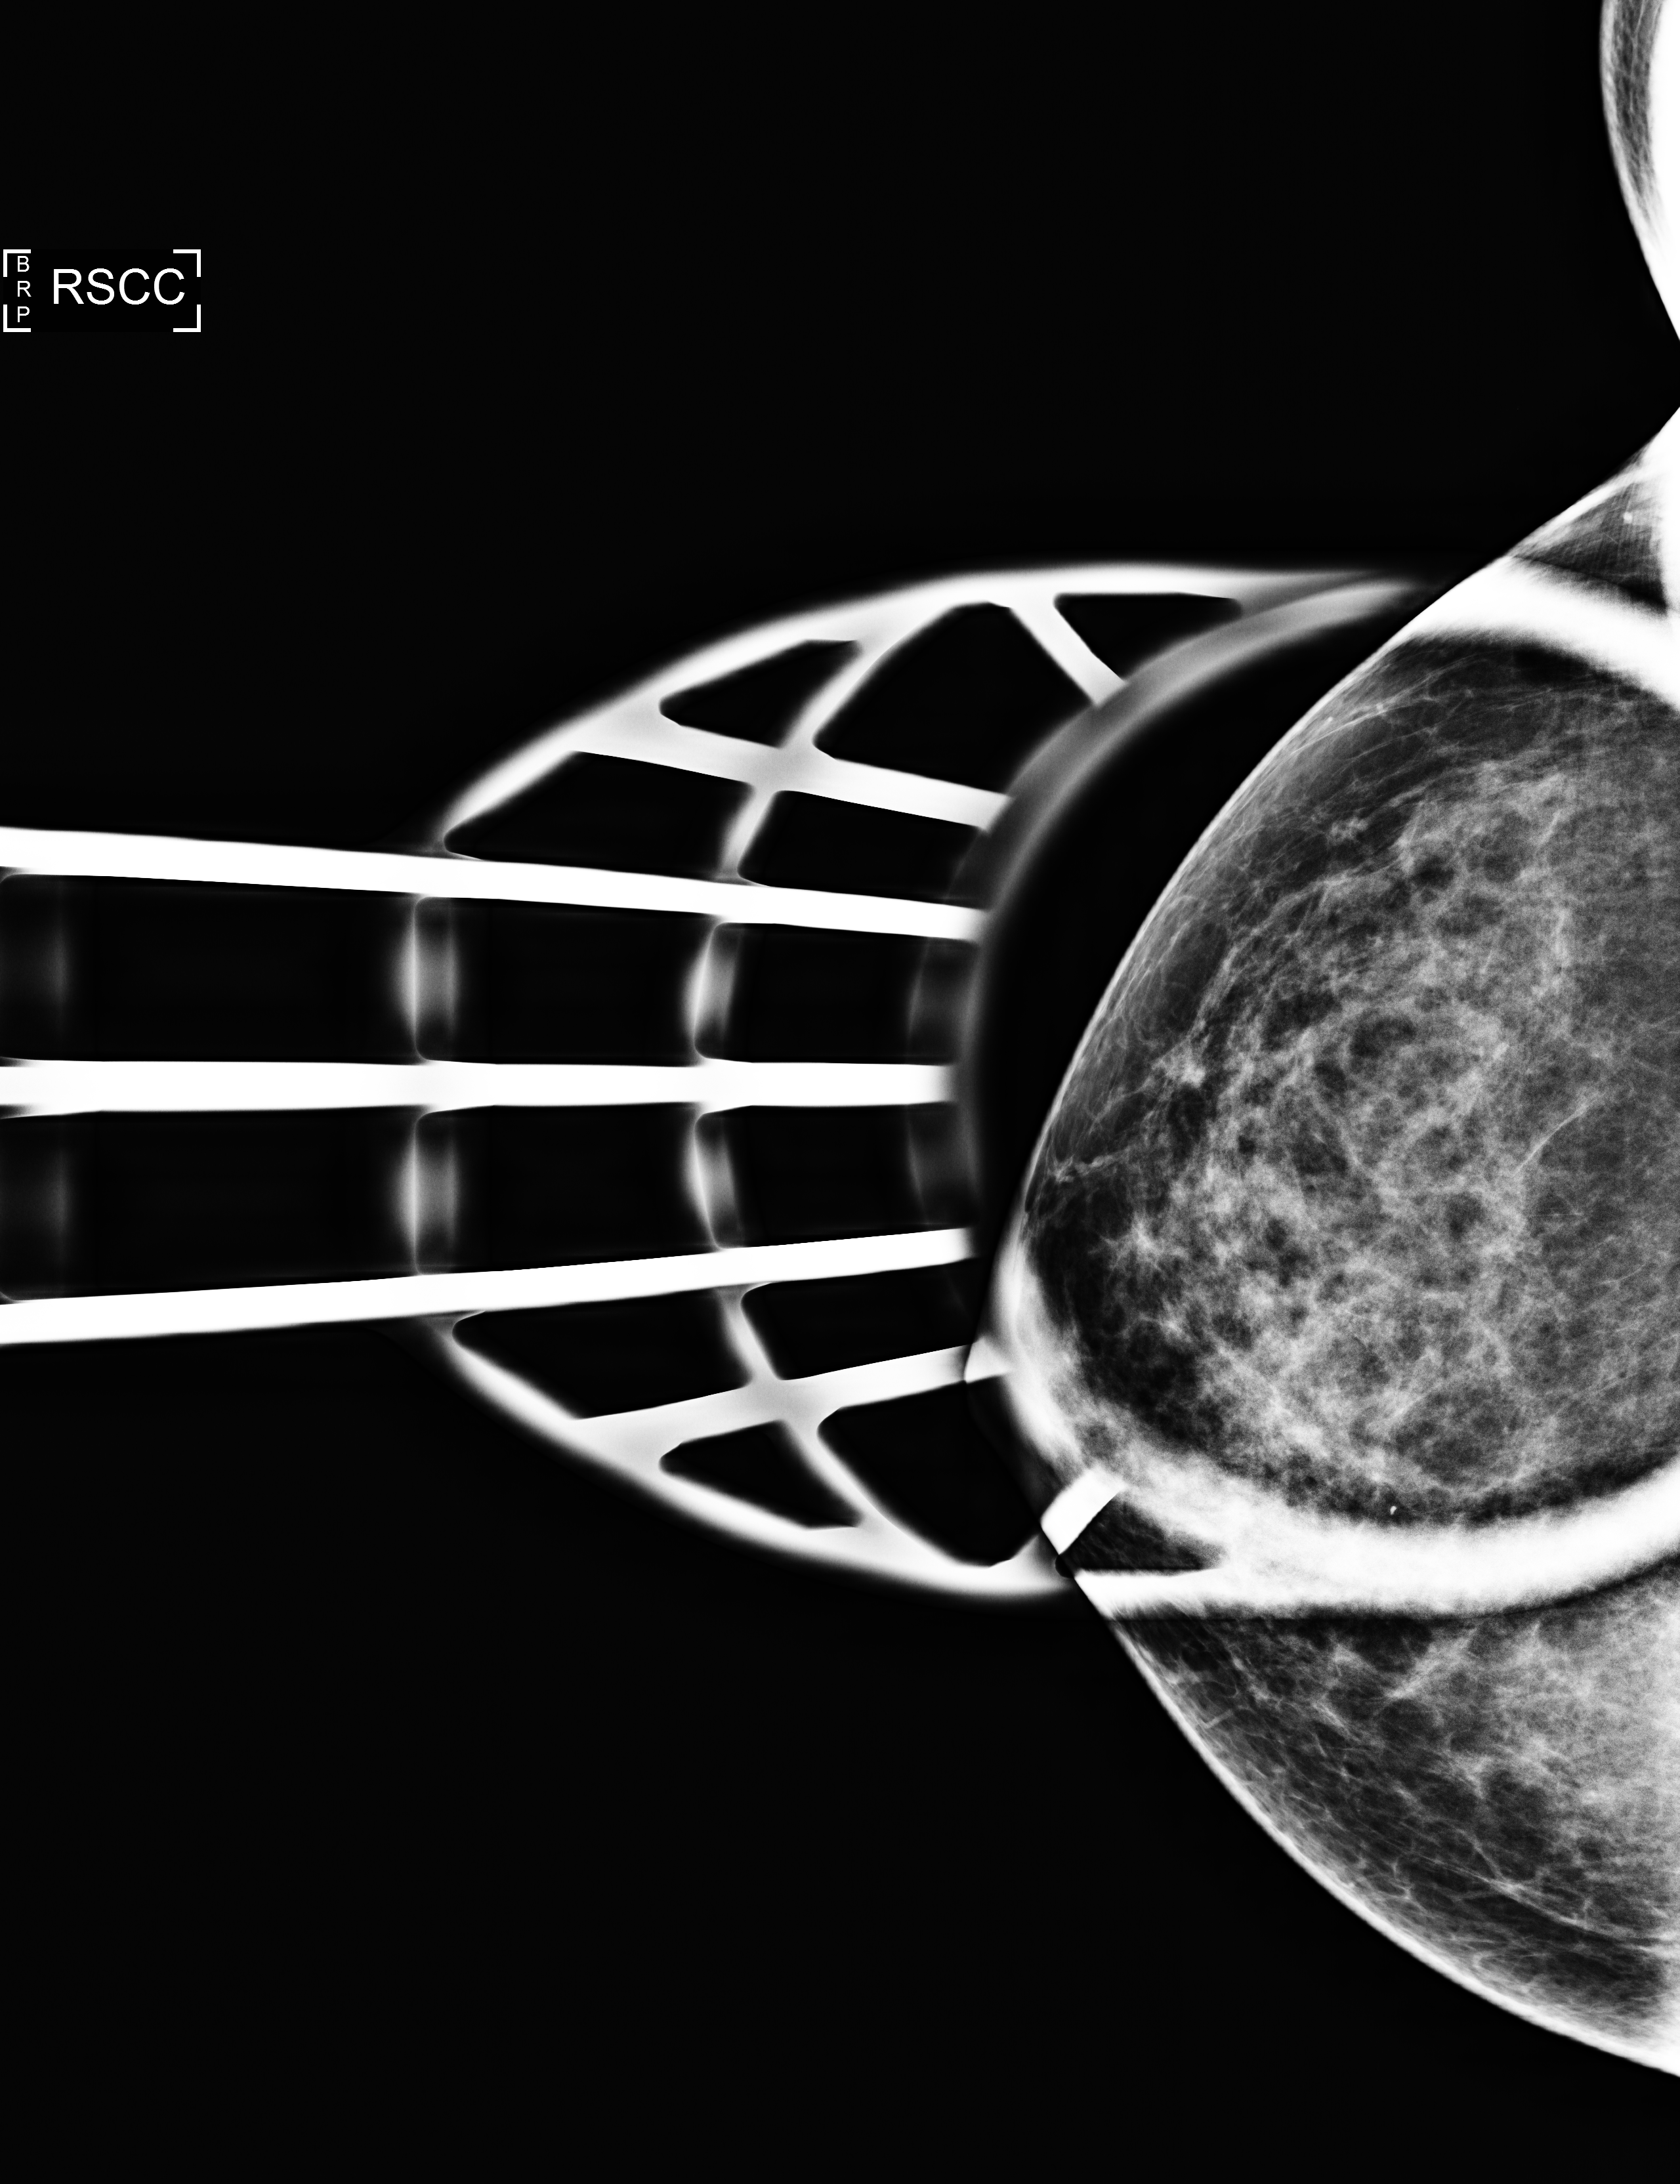
Digital mammogram (FFDM); right breast; cranio-caudal projection (spot compression); screening examination. Patient: female, 63 years.
- BI-RADS breast density category at the screening exam (both breasts, scale 1–4): 3
- final BI-RADS assessment for this screening round (tomosynthesis exam, both breasts): category 2
- recall: no recall after this screen